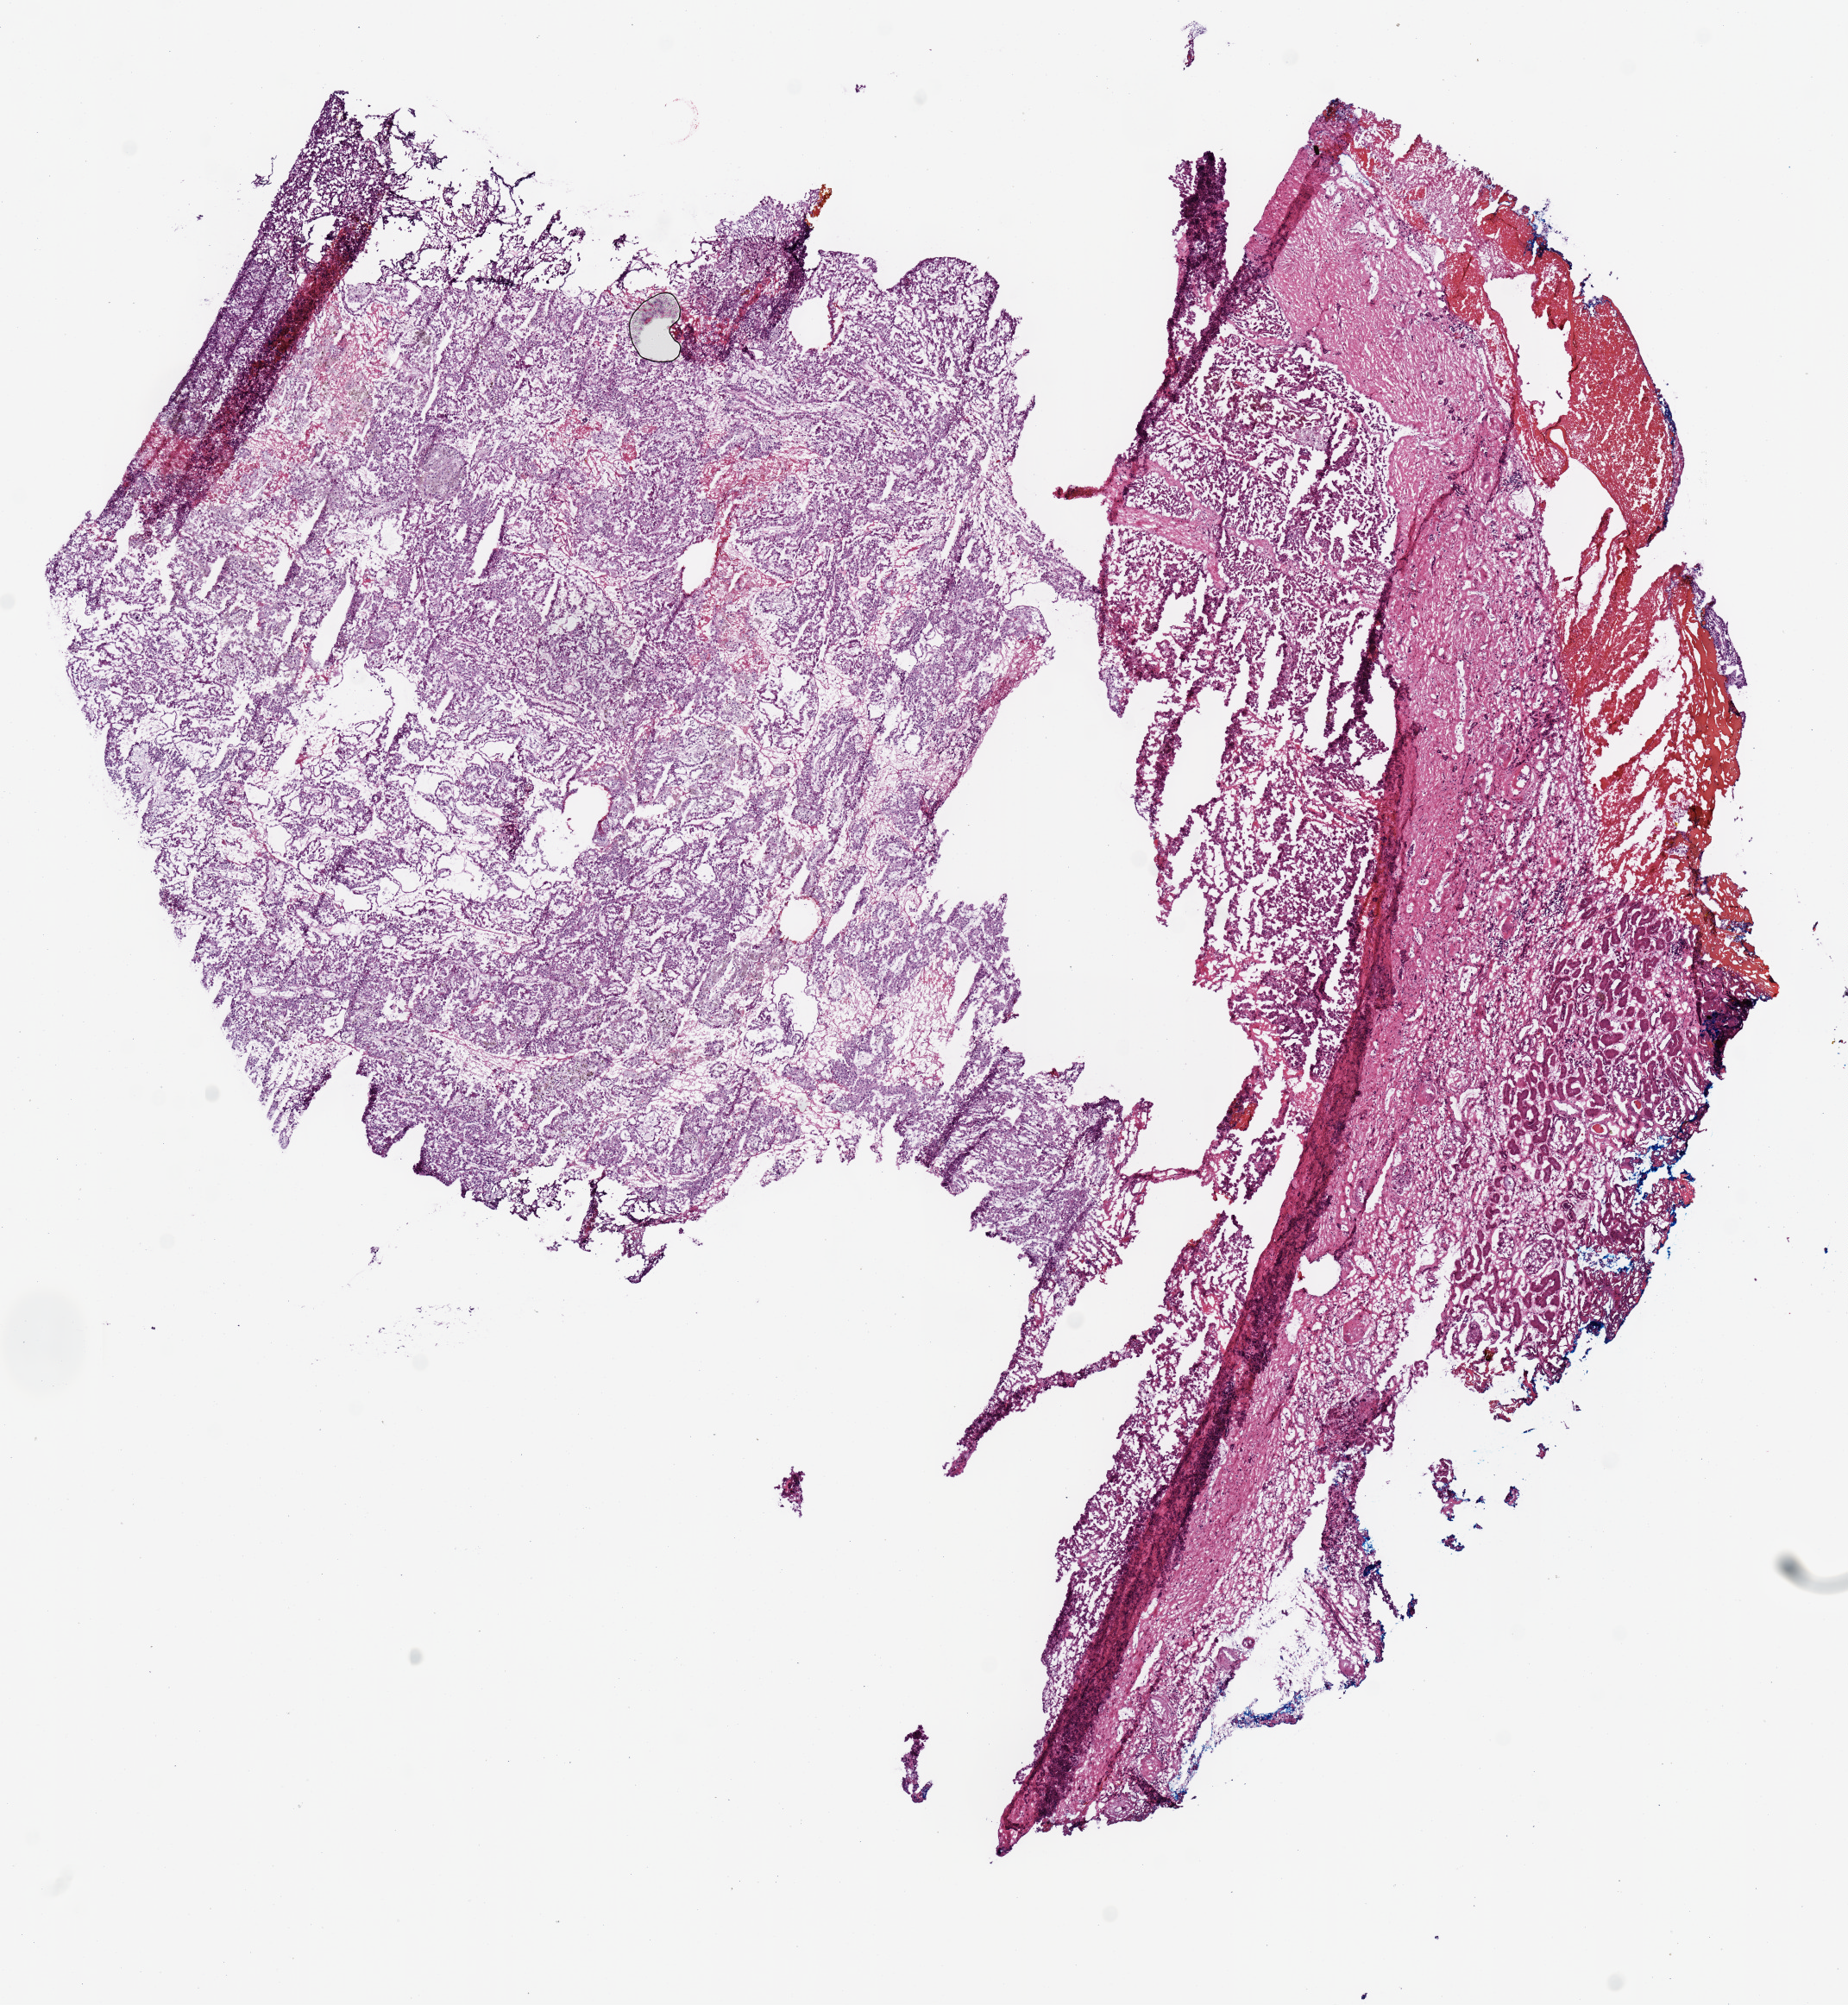
H&E-stained whole-slide image, shown as a low-resolution overview of the whole scanned area (about 8.5 x 9.2 mm, from a 20x scan). Frozen section from the top of the tissue portion. Kidney, primary tumour sample. Male patient; age at initial diagnosis 71 years. Pathologist review of this section (percent, as recorded): tumour nuclei 70%, necrosis 0%.
Pathologic diagnosis: Papillary adenocarcinoma, NOS.